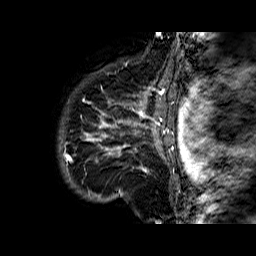
Breast MRI (dynamic contrast-enhanced), one sagittal slice; slice 56 of 60 in the series (ordered by position); dynamic contrast-enhanced series, time point 2 of 6 at this slice position (early post-contrast); 1.5 T; TE 6.3 ms, TR 32.4 ms; 4 mm slice thickness; 256 × 256 image matrix. Female patient. From the clinical record (not read from this slice): setting: breast cancer imaged before/during neoadjuvant chemotherapy; receptor status: HR-positive, HER2-negative.
Outlined on this slice (semi-automatic segmentation, software-assisted and operator-edited):
- analysis volume of interest (the breast-tissue region the enhancement analysis was run in; not a lesion): bounding box <68,72,177,183> (left, top, right, bottom; pixels)
- tumour enhancement mask (voxels above the 100 % enhancement threshold inside the analysis volume of interest): <68,82,174,172>